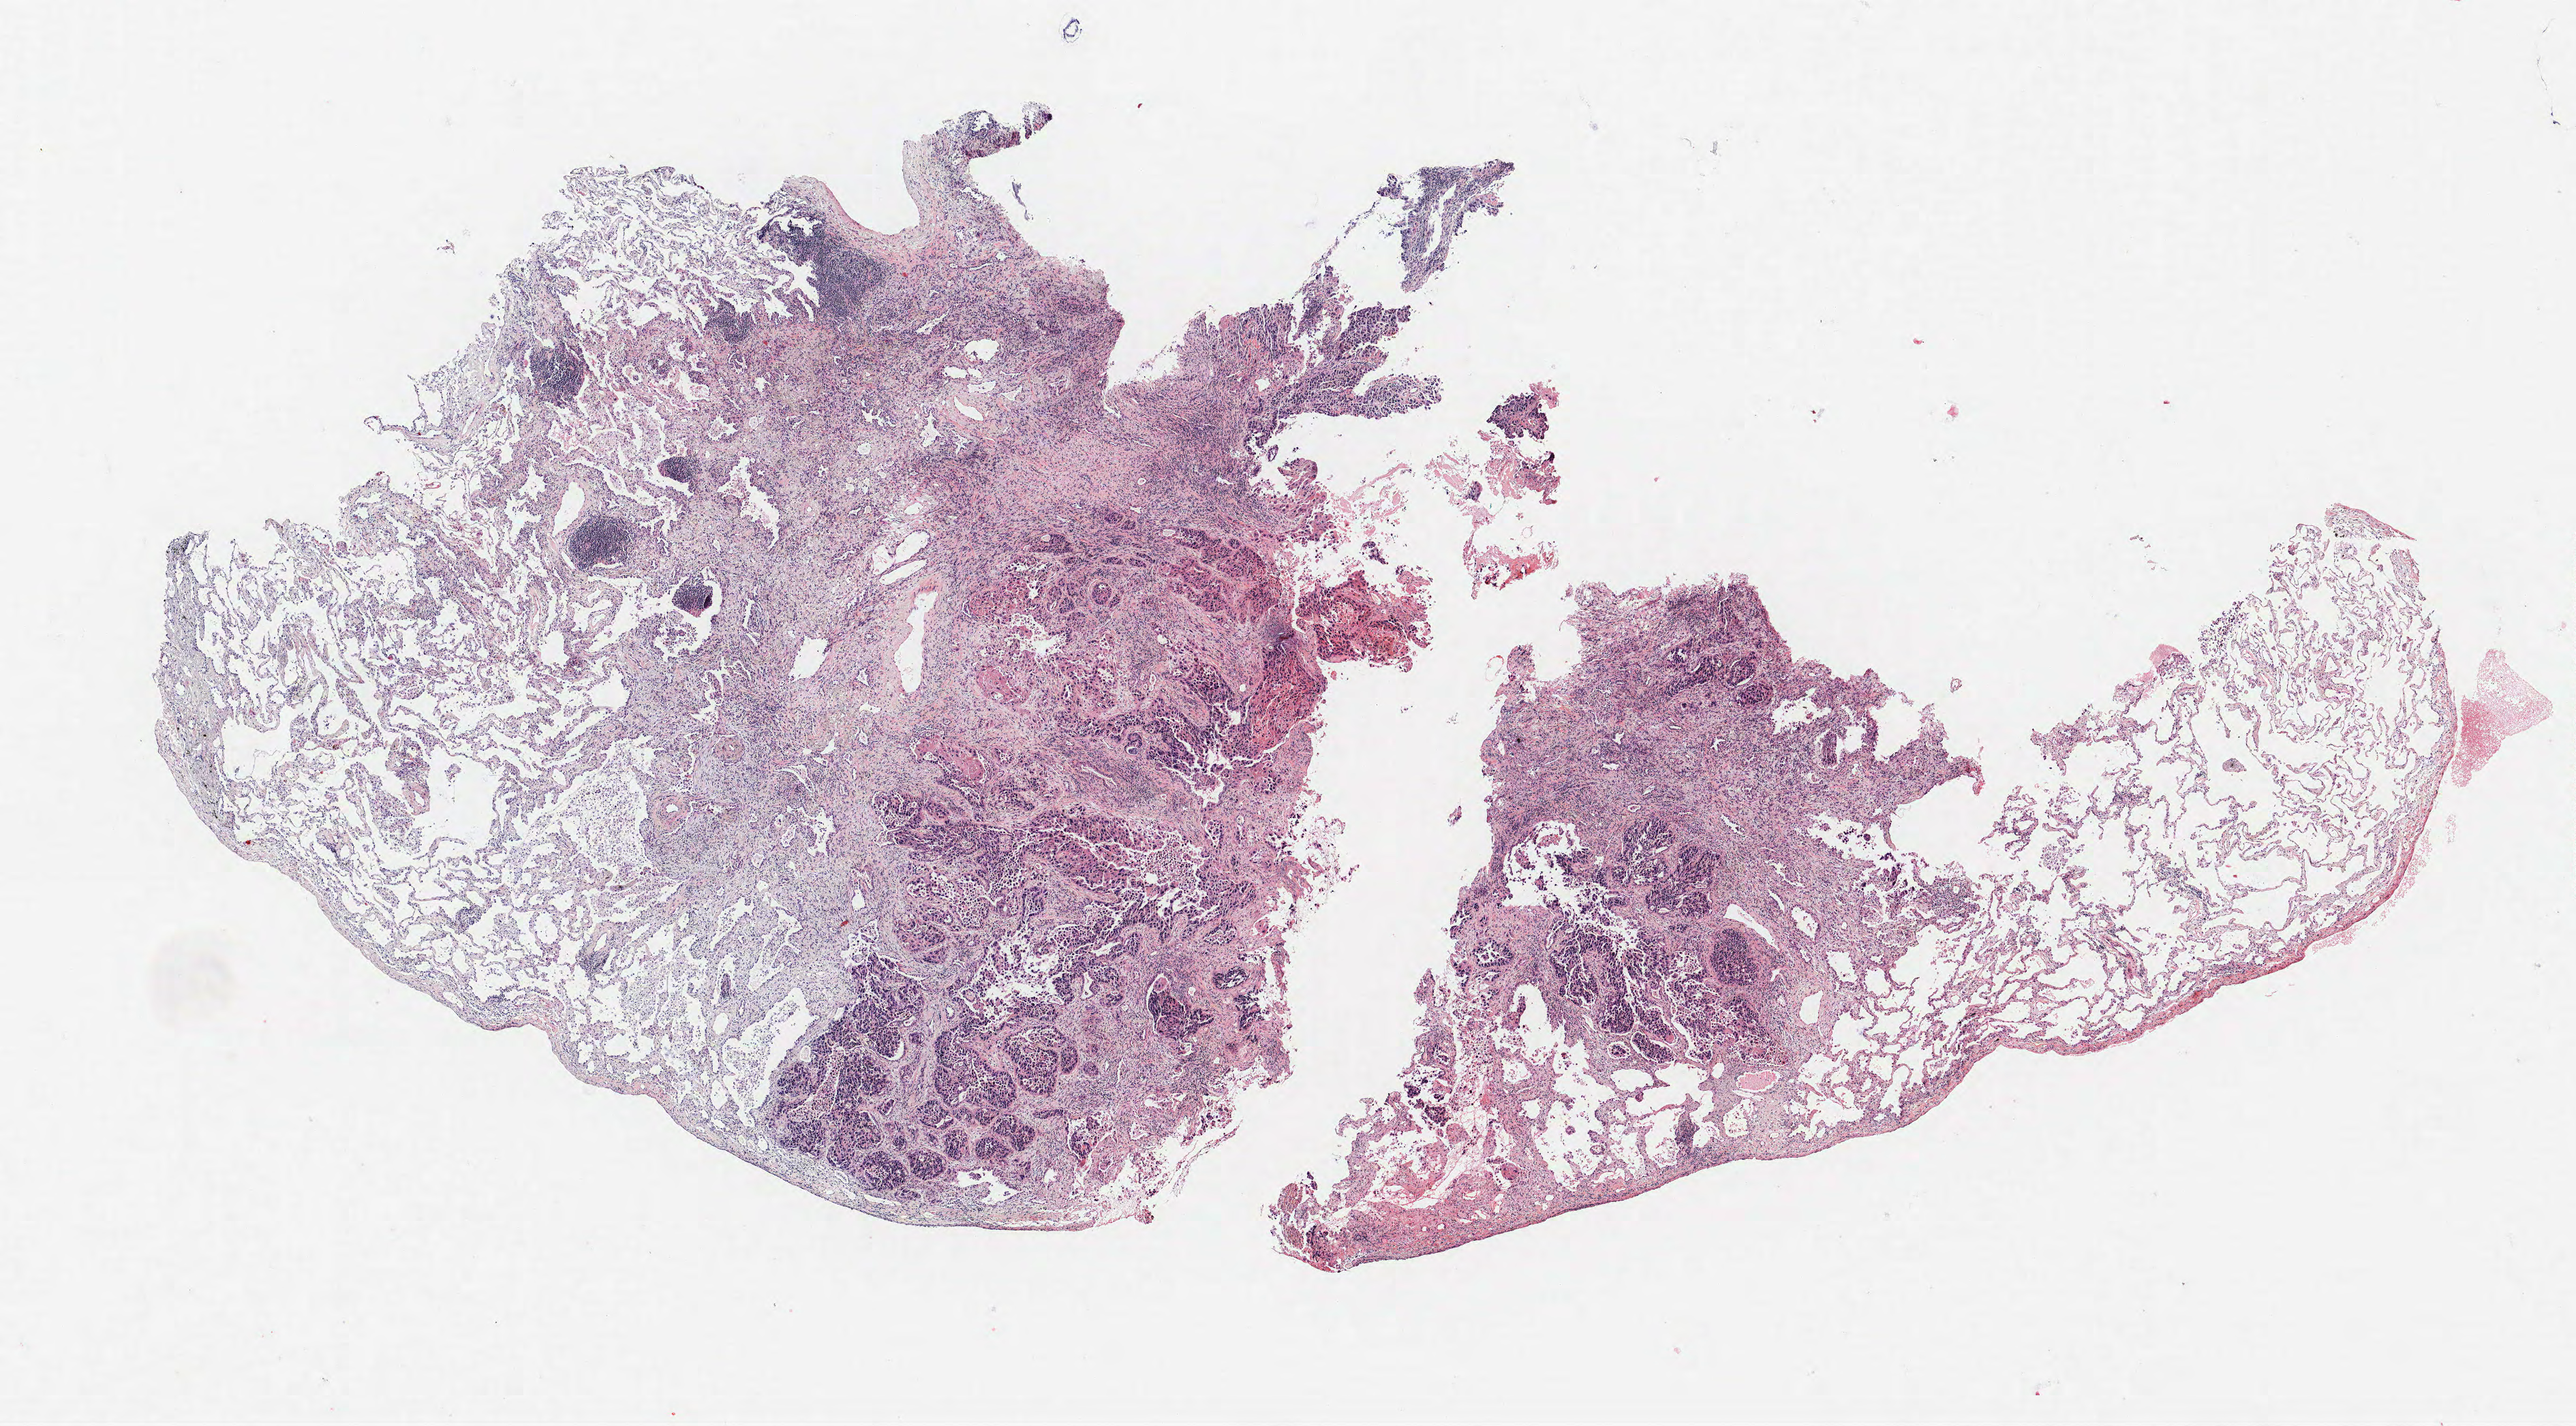
H&E whole-slide image, low-resolution overview of the scanned area, about 15.1 x 8.4 mm. FFPE section. Lung. Female, age 63 at enrolment.
Participant's lung-cancer diagnosis: Squamous cell carcinoma, NOS.